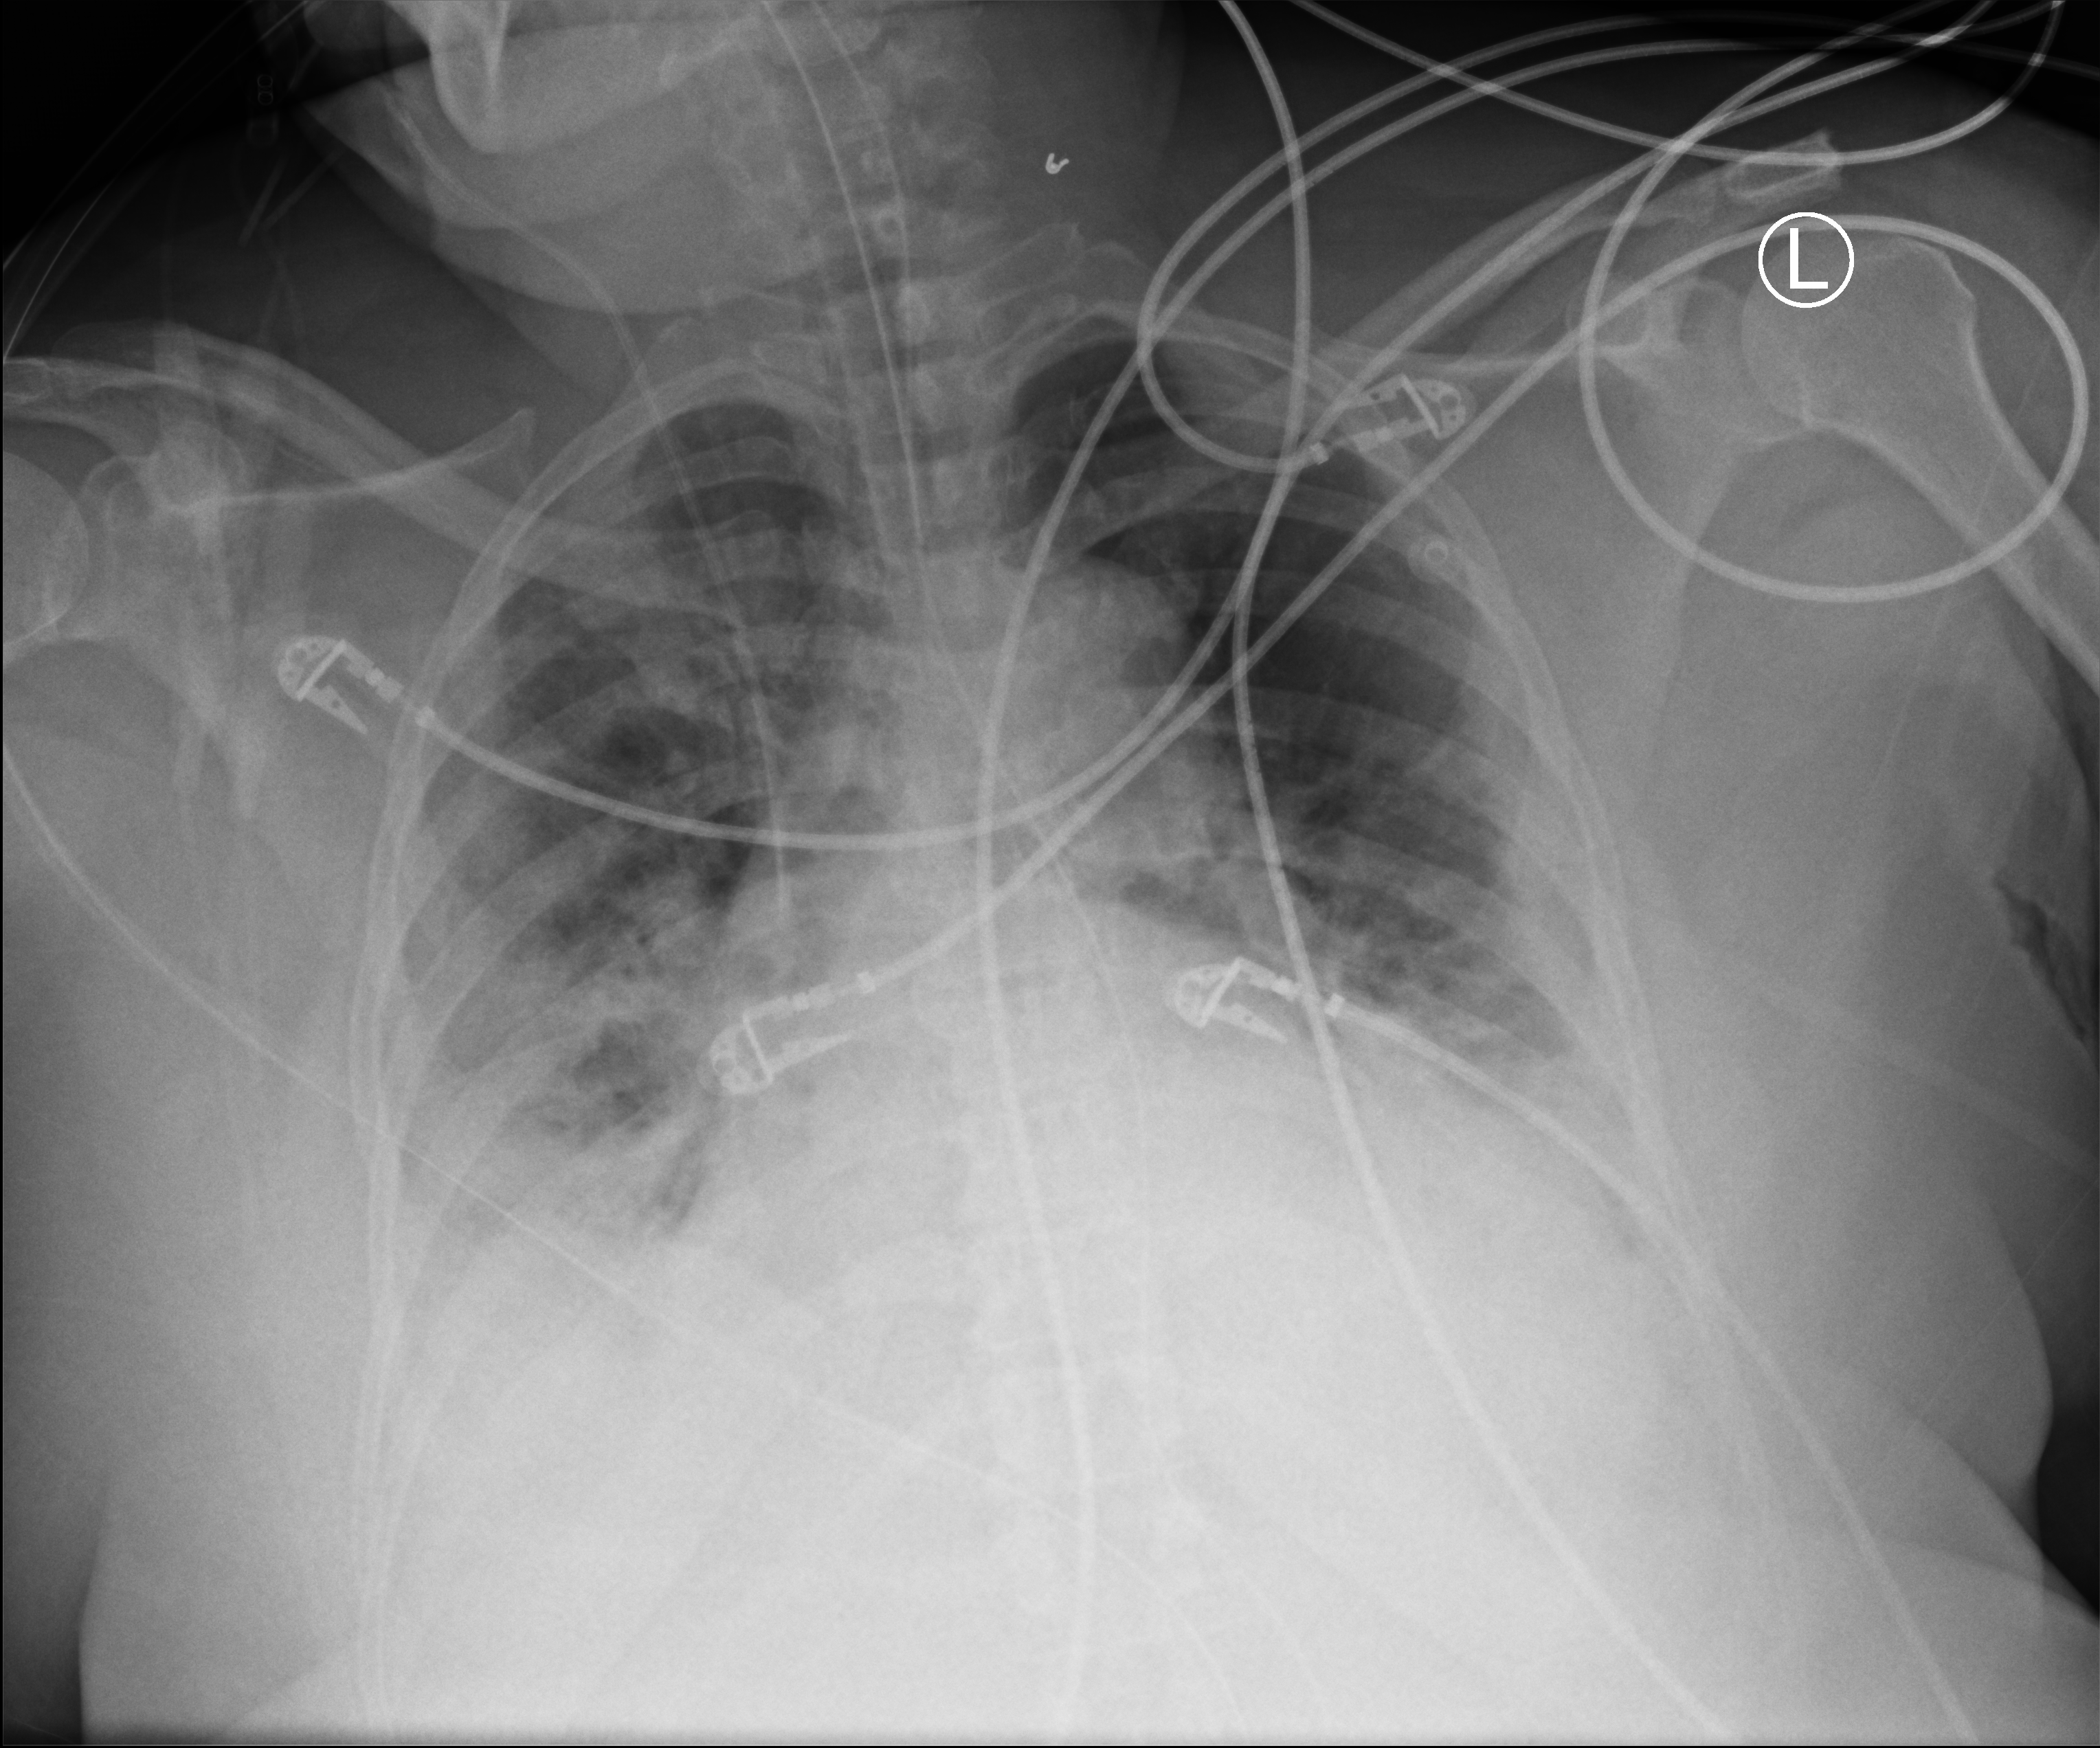
Portable chest radiograph; anteroposterior (AP) projection. Patient hospitalised with COVID-19; female, aged 60–74 years.
Hospital-stay facts (about this admission, not read from this image; timing relative to this image not recorded):
- hypertension (admission record): yes
- chronic kidney disease (admission record): no
- admitted to intensive care during this hospital stay: yes